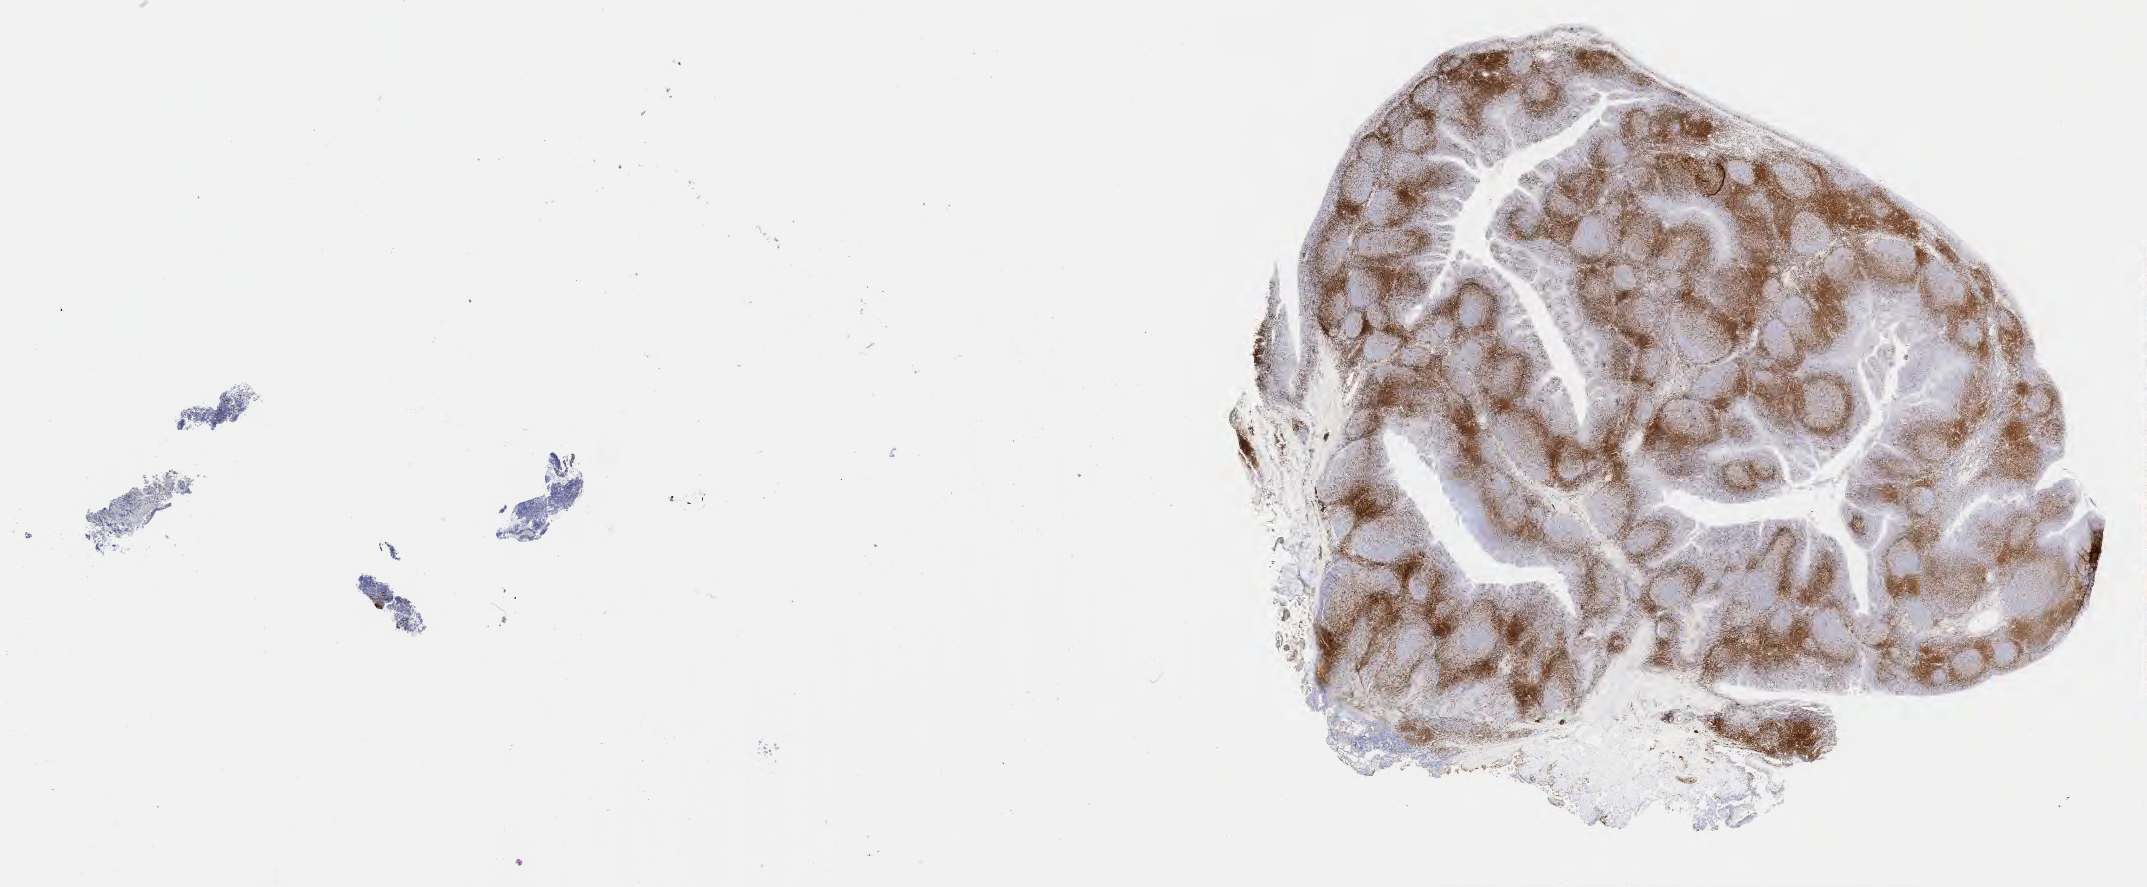
IHC for CD3, whole-slide image, a low-resolution overview of the entire scanned area, about 34.7 x 14.3 mm. Tumor tissue. Anatomic site: lymph node of head and neck. Patient: female, age at initial diagnosis 4 years.
- histologic diagnosis: Burkitt lymphoma, NOS